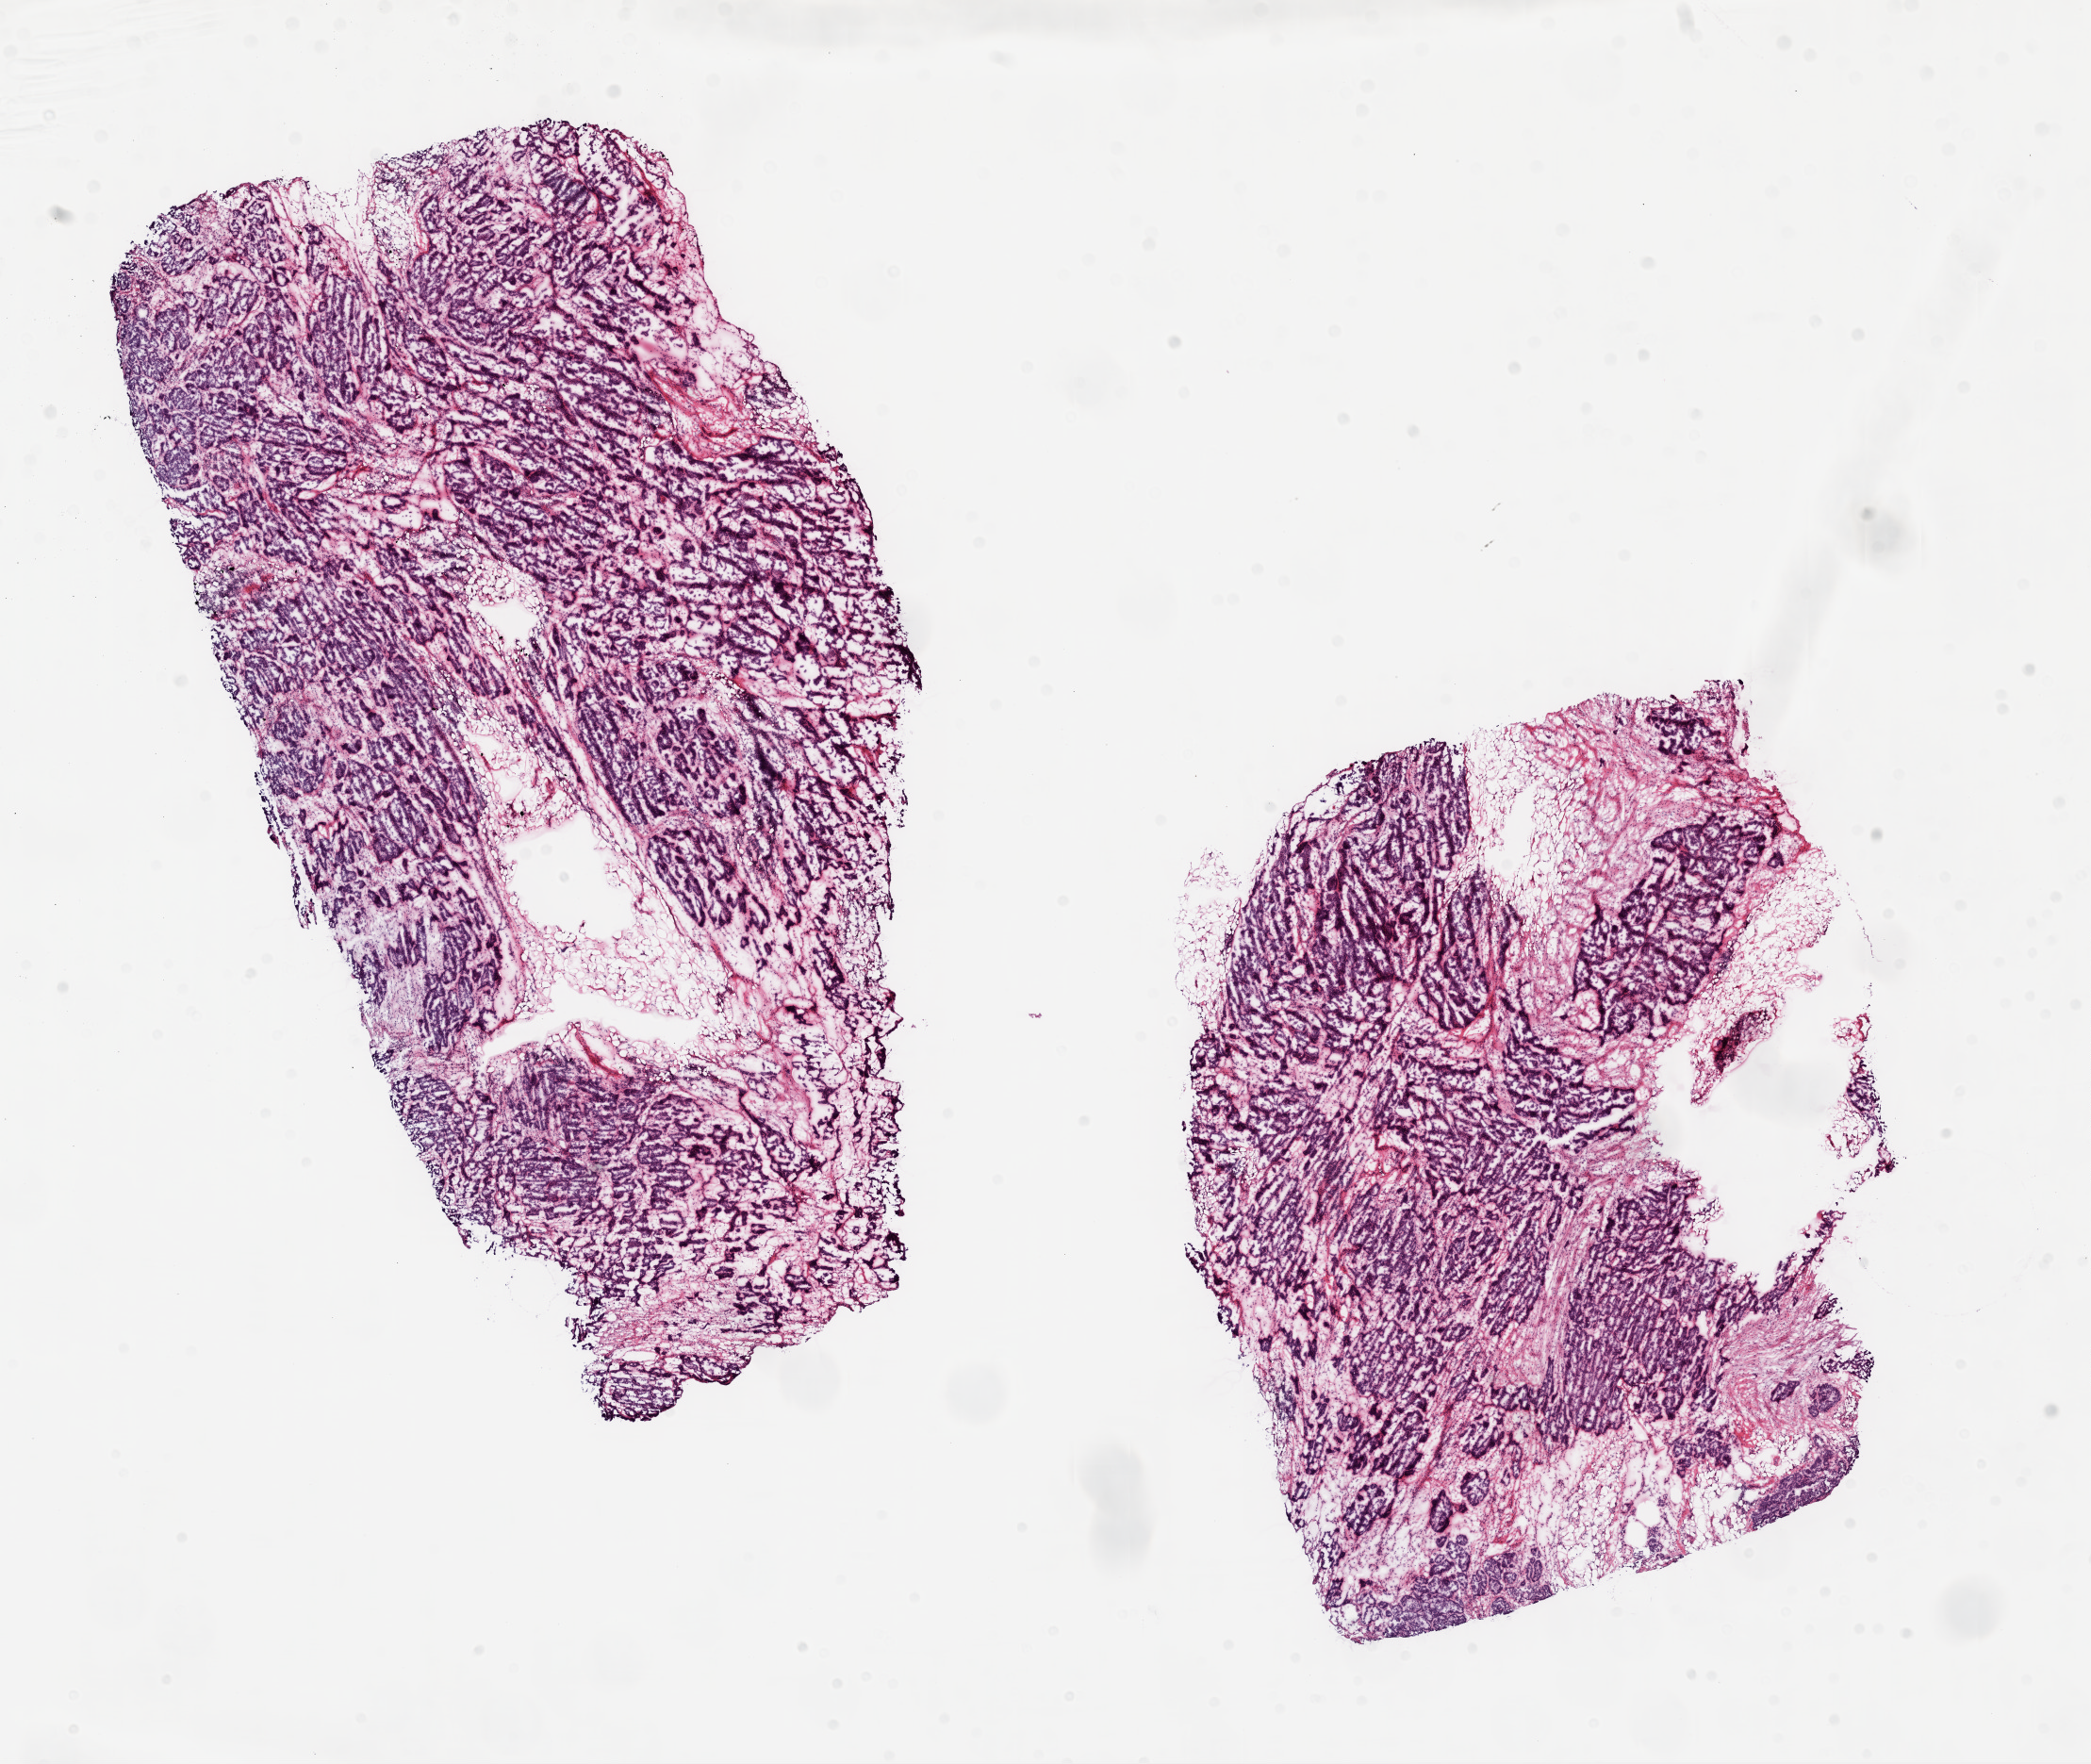
Whole-slide histology image, Hematoxylin and eosin (H&E) stained, low-resolution overview of the scanned area, about 17.9 x 15.1 mm; frozen section; sample: primary tumour, ovary. Female, age 58 years at initial diagnosis. Histologic grade: G3 (poorly differentiated). Slide review estimates, as recorded: tumour cells 90%, tumour nuclei 95%, normal cells 0%, stromal cells 10%, necrosis 0%. Inflammatory infiltration, as recorded: lymphocyte infiltration 90%.
• laterality: bilateral
• FIGO stage: IIIC
• pathologic diagnosis: Serous cystadenocarcinoma, NOS